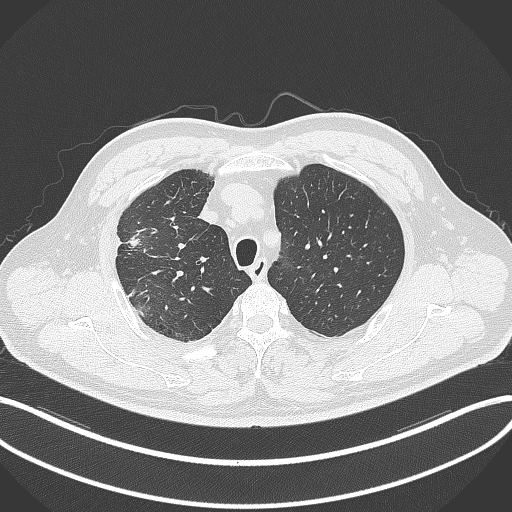
Chest CT, one axial slice. Slice 275 of 348 in the series (ordered by position). 120 kVp. Lung window (W 1500 / L -600 HU). 1 mm slice thickness. 512 × 512 image matrix, field of view 400 × 400 mm. Male patient, age 55 years. Case-level facts recorded for this patient, not image findings: clinical TNM (as recorded): T3 N2 M1.
Annotated regions visible in this slice (bounding box drawn by a radiologist):
- lung tumour (recorded histology: adenocarcinoma): bounding box <125,233,143,253> (left, top, right, bottom; pixels)